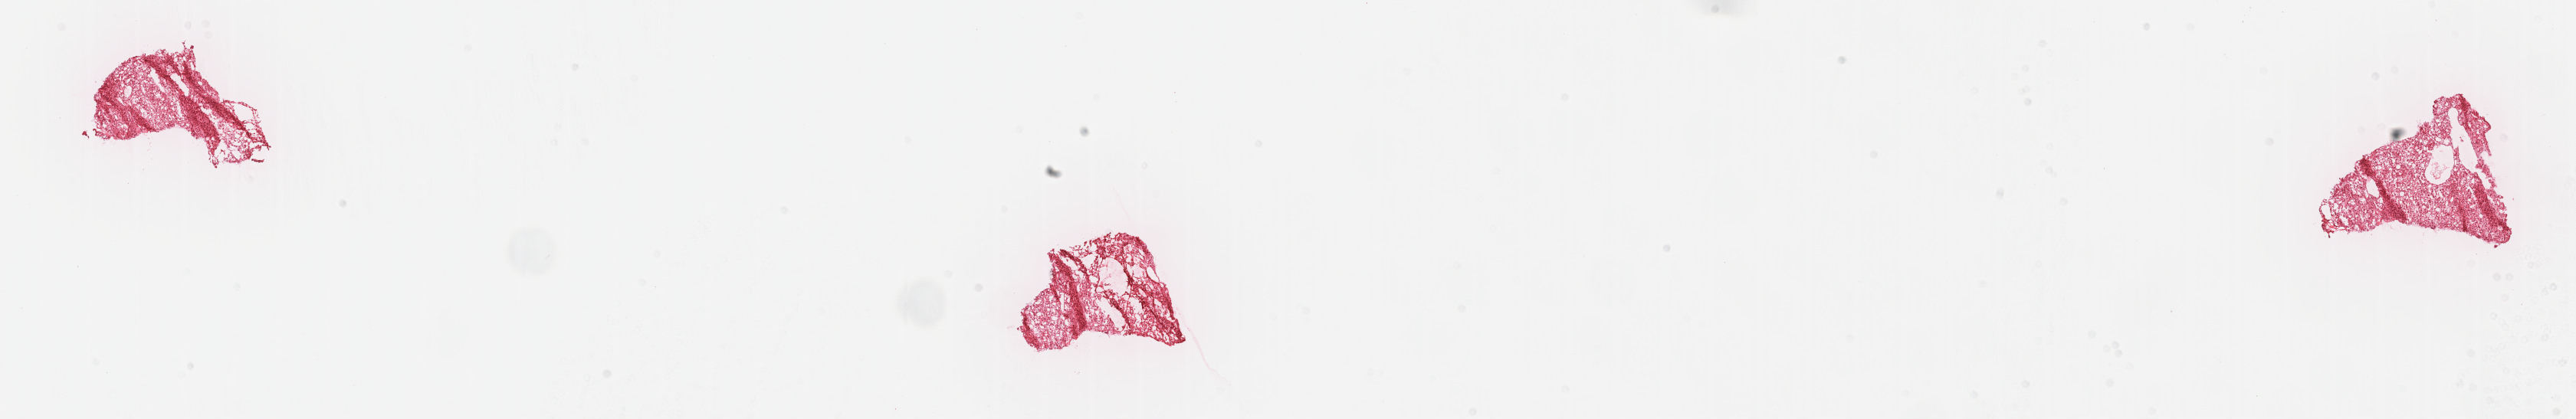
Whole-slide histology image, H&E, whole scanned area (about 27.2 x 4.4 mm) shown as a low-resolution overview; frozen section from the top of the tissue portion; primary tumour sample from the liver. Female patient; age at initial diagnosis 79 years. Histologic grade: G1 (well differentiated). Slide review estimates, as recorded: tumour cells 80%, tumour nuclei 80%, normal cells 0%, stromal cells 20%, necrosis 0%. Inflammatory infiltration, as recorded: lymphocyte infiltration 3%, monocyte infiltration 1%, neutrophil infiltration 2%.
* AJCC pathologic stage: II (7th edition)
* diagnosis: Hepatocellular carcinoma, NOS